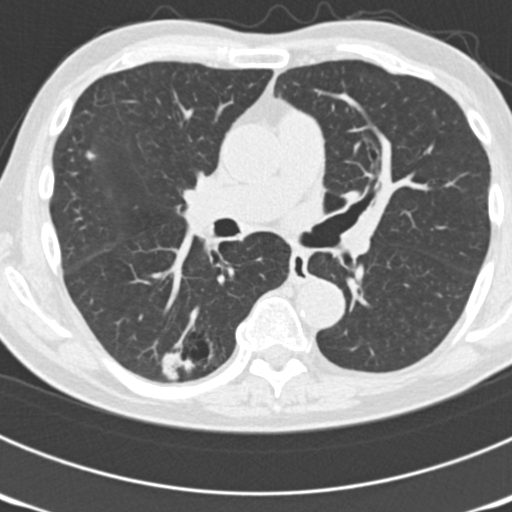
Low-dose screening chest CT, axial slice; third annual screen; lung window (W 1500 / L -600 HU). Male, age 70 years at enrolment.
Lesion marked by an expert reader, bounding box <145,307,237,385> (left, top, right, bottom; pixels). The screening reader recorded 3 non-calcified nodules or masses ≥4 mm on this exam (right upper lobe, left upper lobe, right lower lobe); which of them this box marks is not recorded.